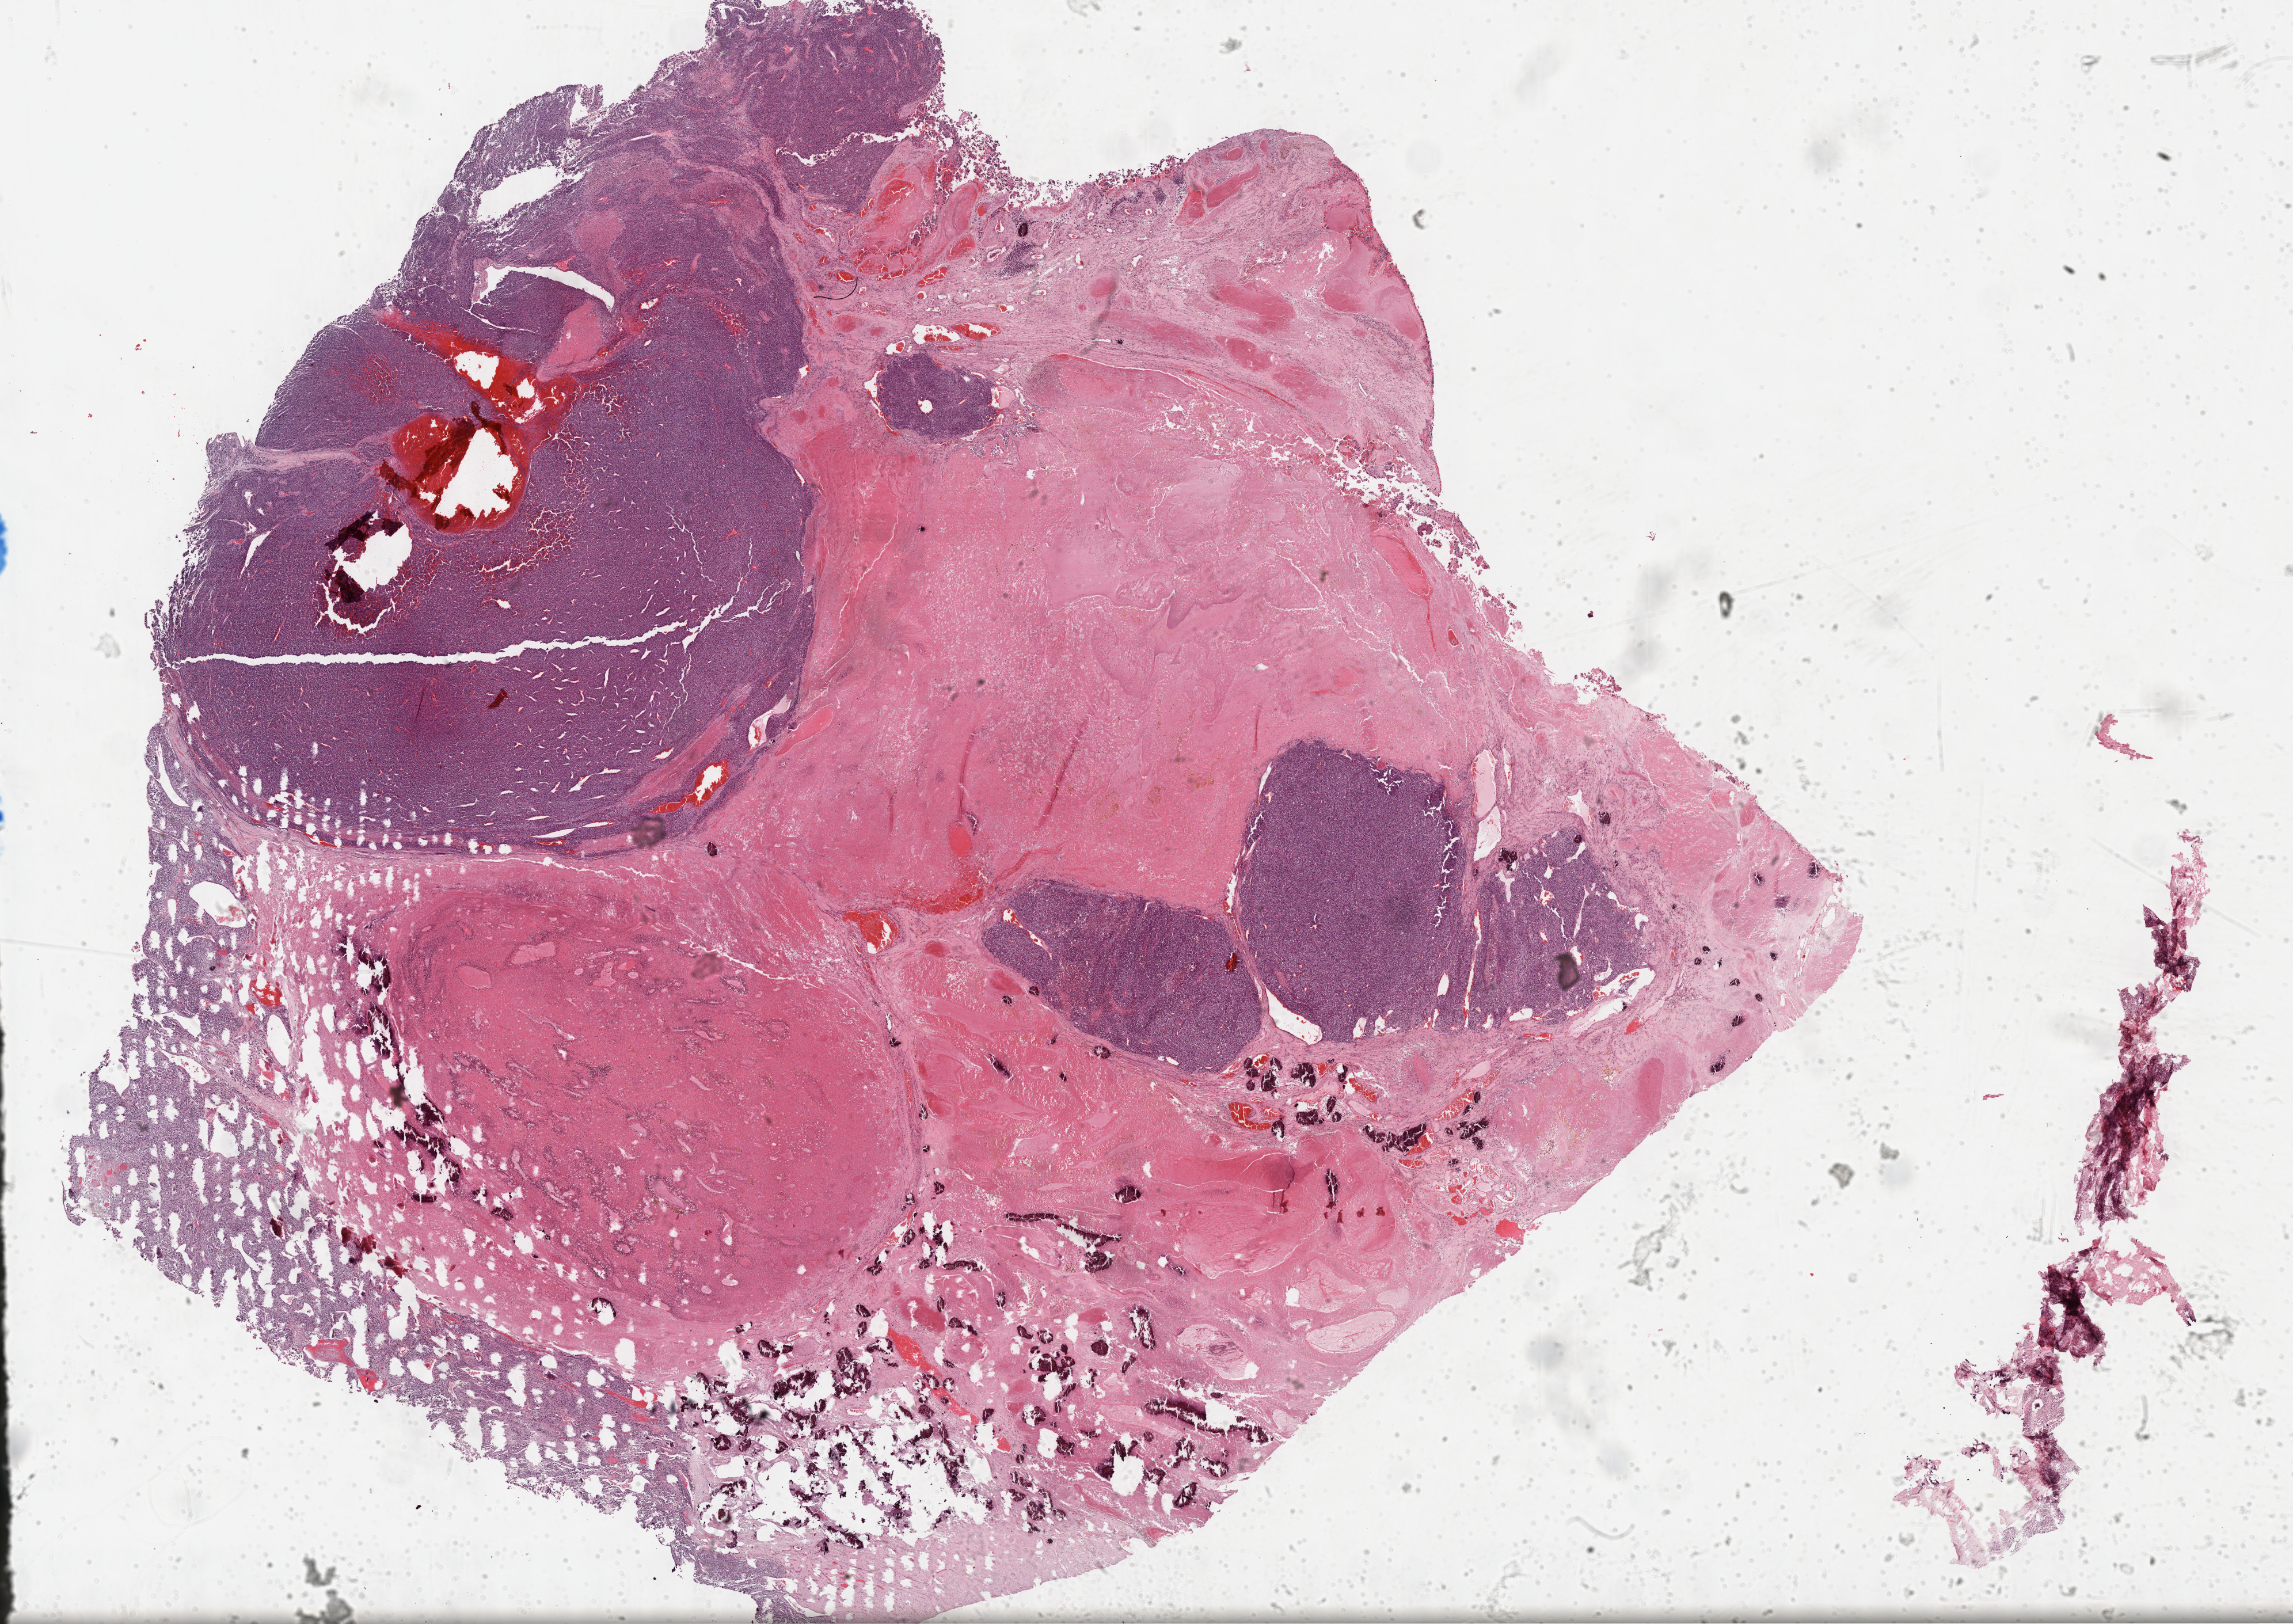
Hematoxylin and eosin (H&E) stained whole-slide image, low-resolution overview of the scanned area, about 32.2 x 22.8 mm; FFPE section; adrenal cortex, primary tumour sample. Female, age 32 years at initial diagnosis.
Lymph nodes positive (case pathology): 0 of 1 examined. Diagnosis: Adrenal cortical carcinoma.